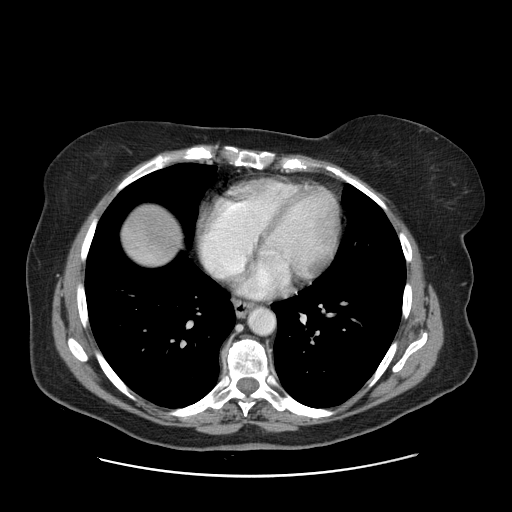
Contrast-enhanced abdominal CT, one axial slice. Slice 153 of 161 in the series (ordered by position). Soft-tissue window (W 400 / L 40 HU). 2.5 mm slice thickness. 512 × 512 image matrix, field of view 398 × 398 mm. Female patient, age 62 years. From the clinical record (not read from this slice): diagnosis: colorectal cancer liver metastases, imaged before liver resection; multiple liver metastases: no; largest metastasis: 2.5 cm; disease in both lobes: no.
Annotated regions visible in this slice (outlined manually by an expert reader):
- liver: bounding box (x1, y1, x2, y2) in pixels: (123, 206, 179, 265)
- planned liver remnant (the part of the liver to remain after resection): (123, 207, 179, 263)